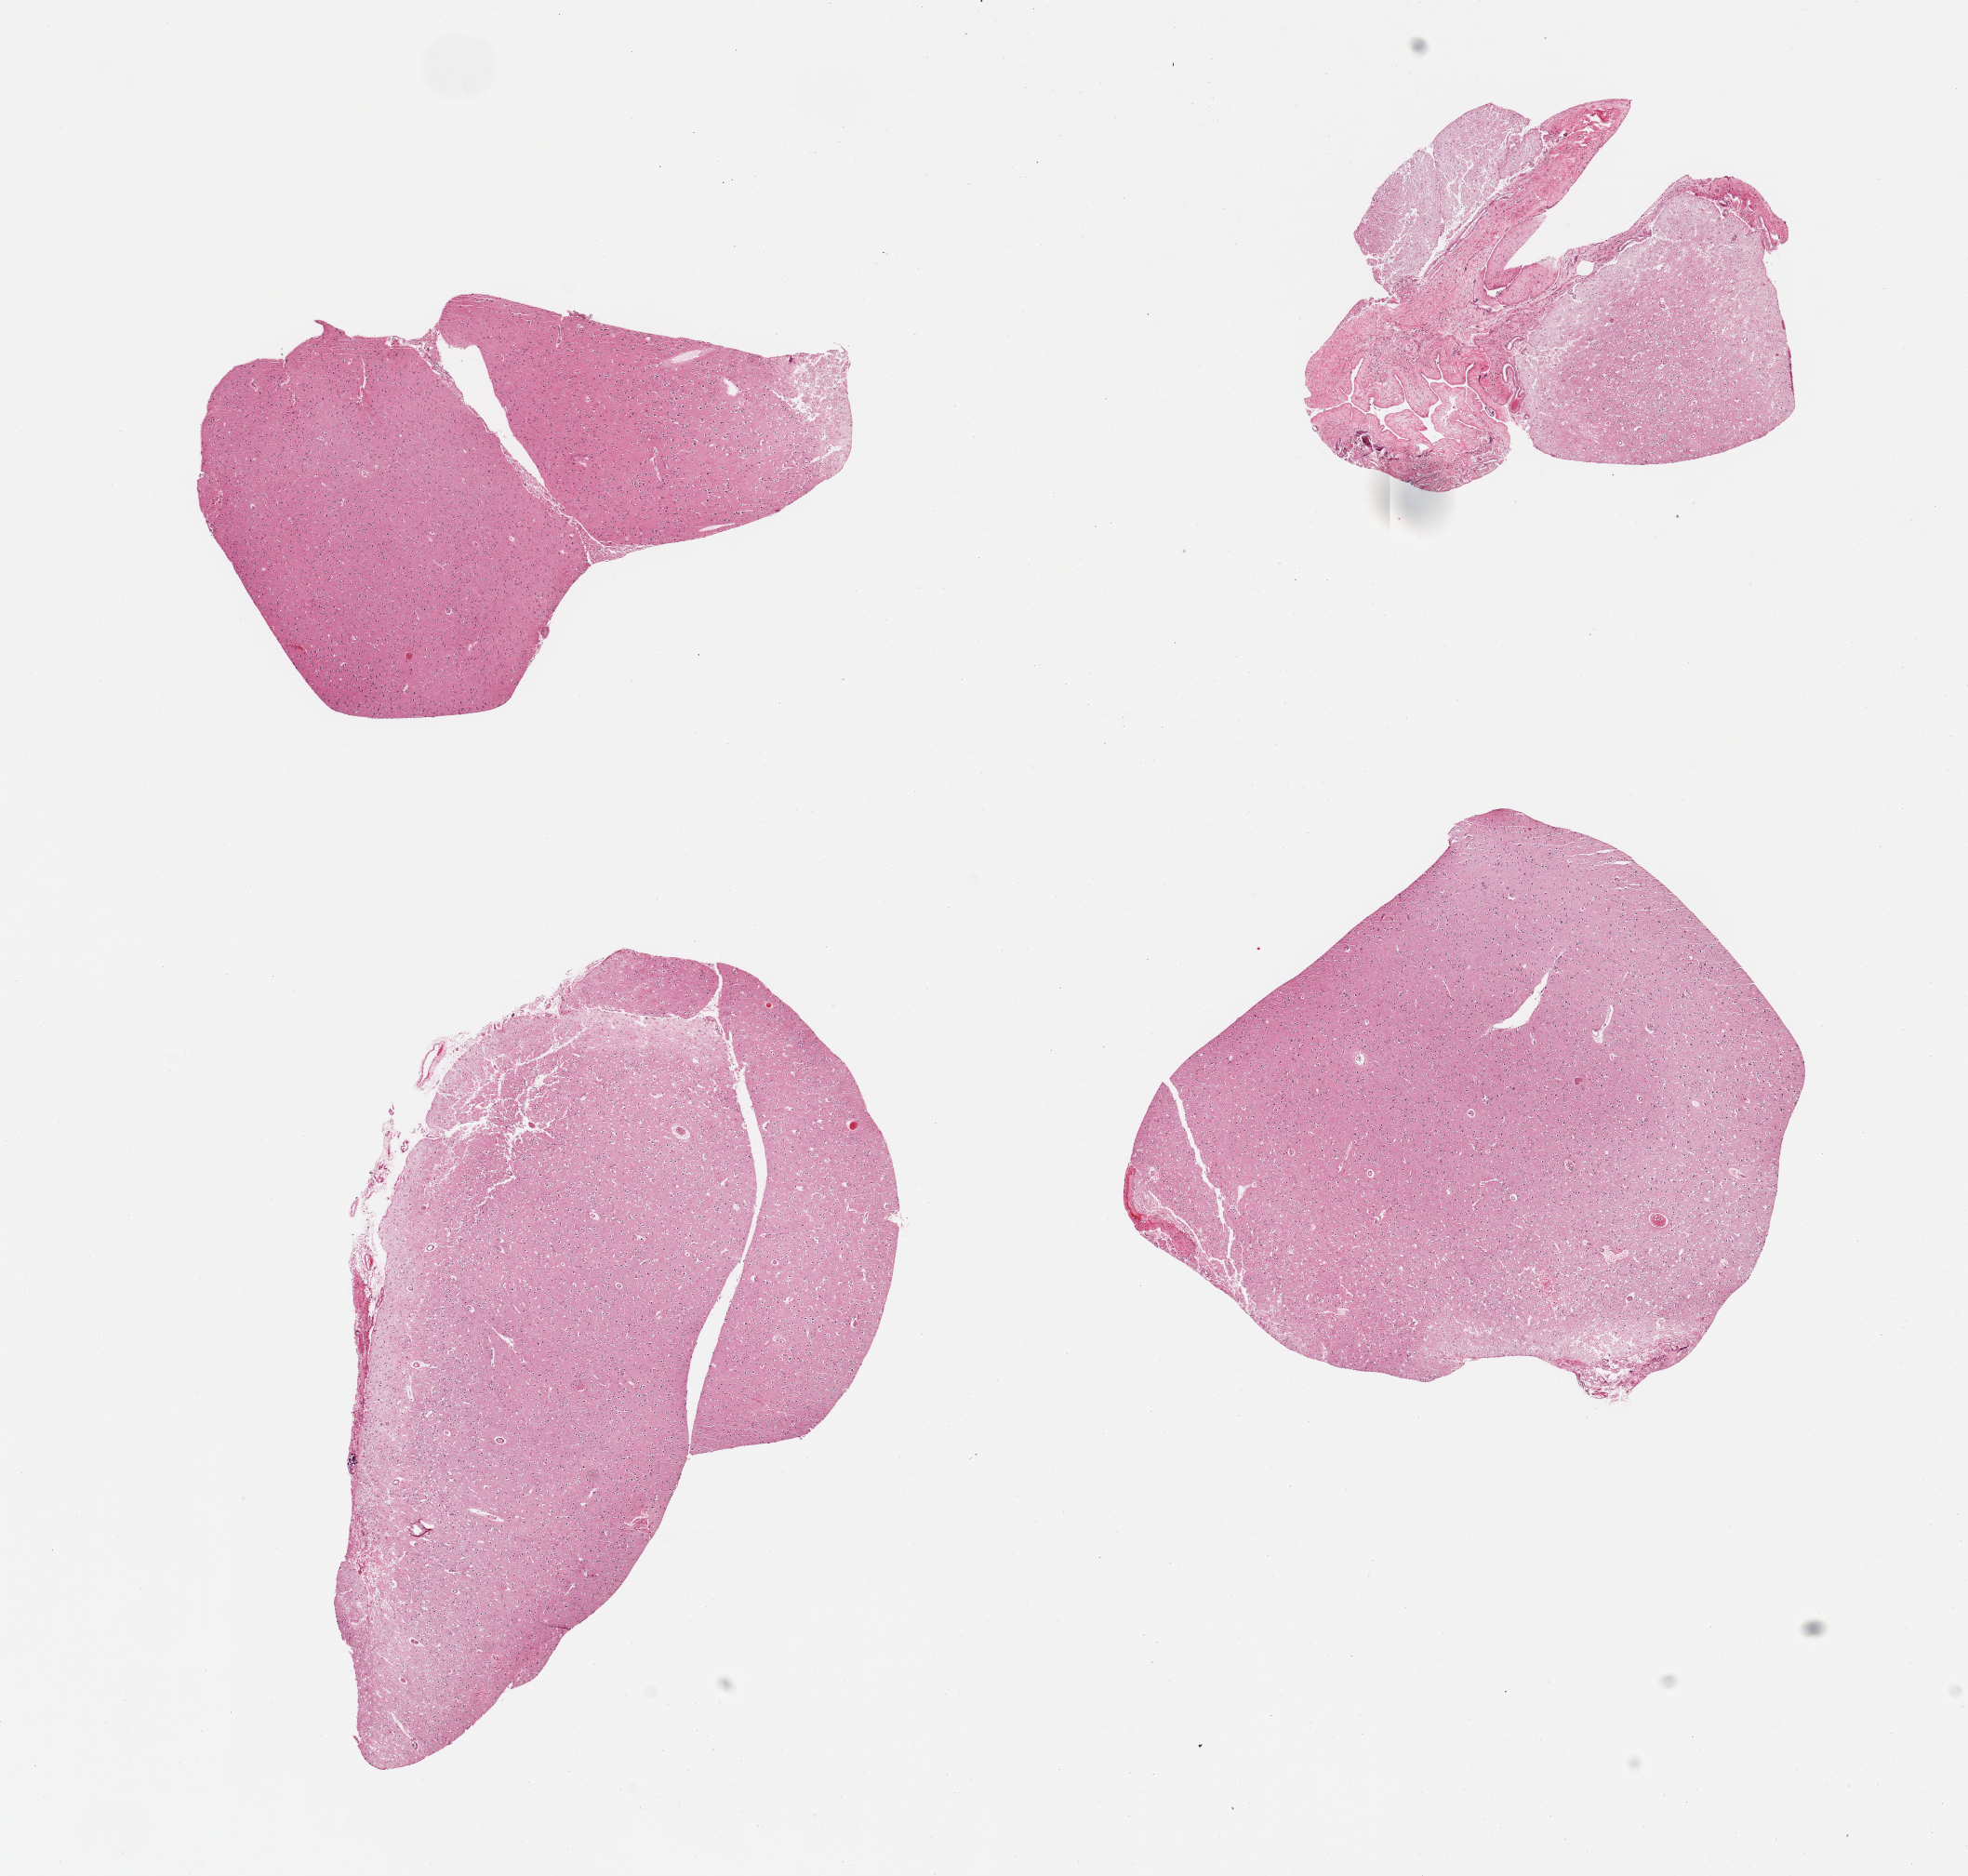
Hematoxylin and eosin (H&E) whole-slide image, brightfield, whole scanned area (about 16.7 x 16.0 mm) shown as a low-resolution overview; PAXgene-fixed, paraffin-embedded tissue; section of cerebral cortex (target tissue); donor tissue sample.
Reviewer comment on this tissue sample: 4 pieces, no abnormalities.